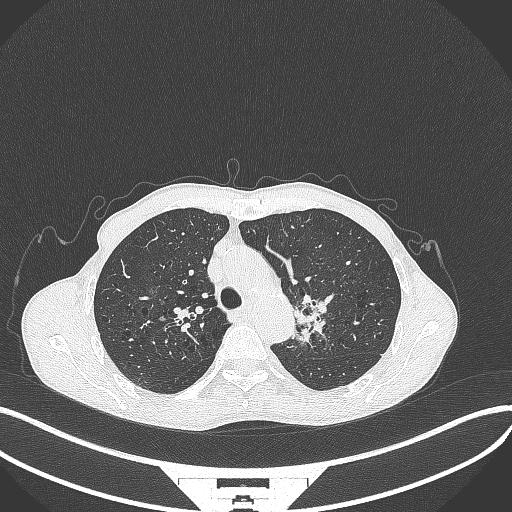
Chest CT, one axial slice; slice 305 of 386 in the series (ordered by position); 120 kVp; lung window (W 1500 / L -600 HU); 1 mm slice thickness; 512 × 512 image matrix, field of view 400 × 400 mm. Male patient, age 65 years. From the clinical record (not read from this slice): clinical TNM (as recorded): T2b N0 M0; histopathological grade: G2.
Annotated regions visible in this slice (bounding box drawn by a radiologist):
- lung tumour (recorded histology: adenocarcinoma): box from (x=290, y=289) to (x=334, y=350) px